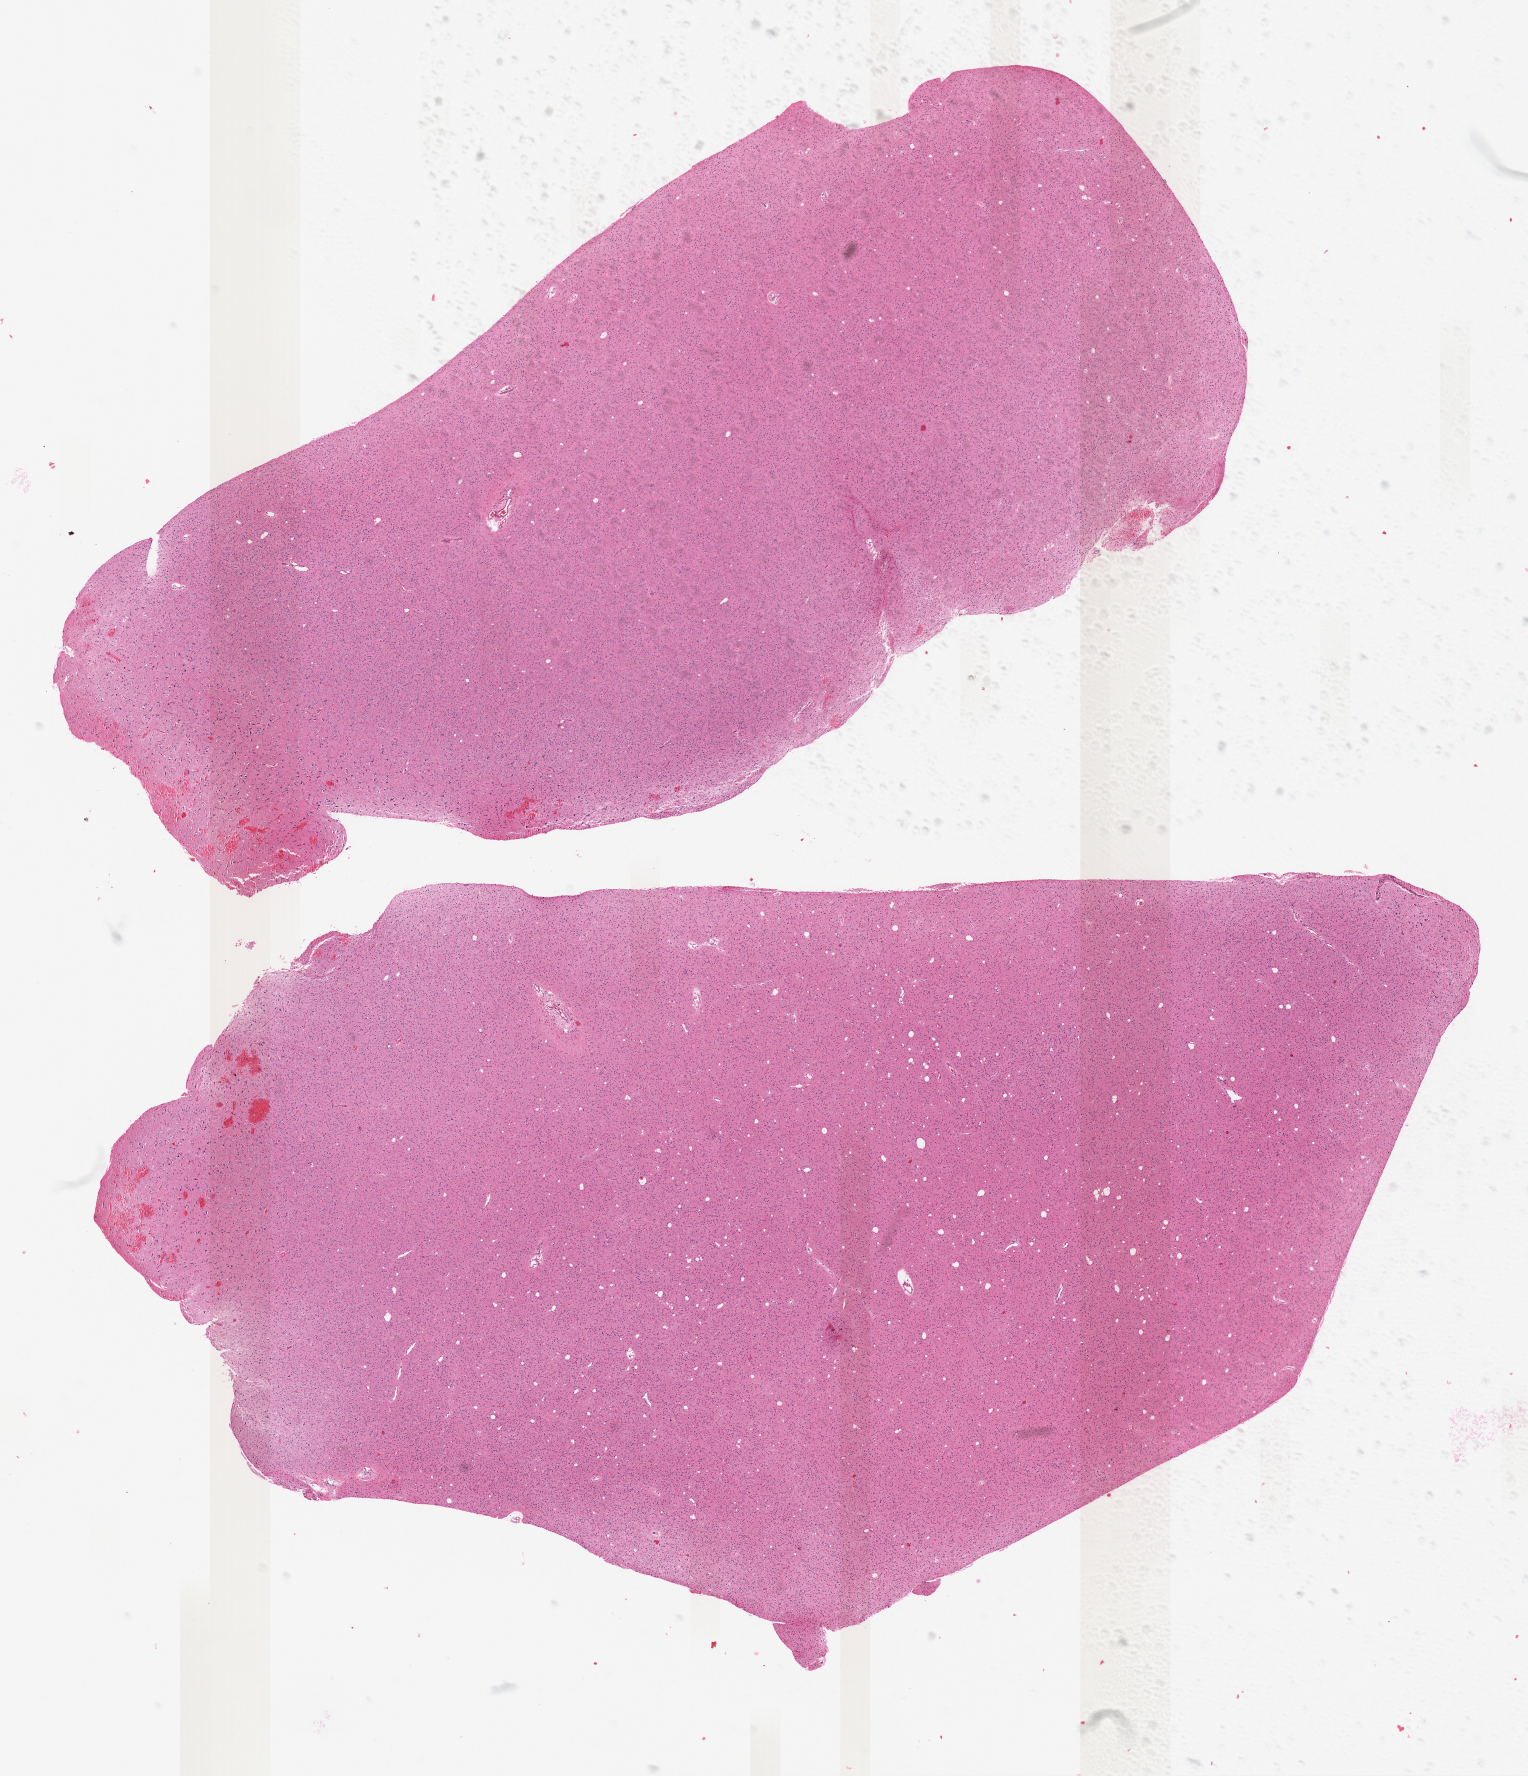
Whole-slide histology image, H&E-stained, shown as a low-resolution overview of the whole scanned area (about 12.3 x 14.3 mm, acquisition: 40x scan); formalin-fixed paraffin-embedded (FFPE) diagnostic section; brain, primary tumour sample. Male, age 31 years at initial diagnosis. Histologic grade: G2 (moderately differentiated).
Laterality: right. Histologic diagnosis: Mixed glioma (cerebrum).